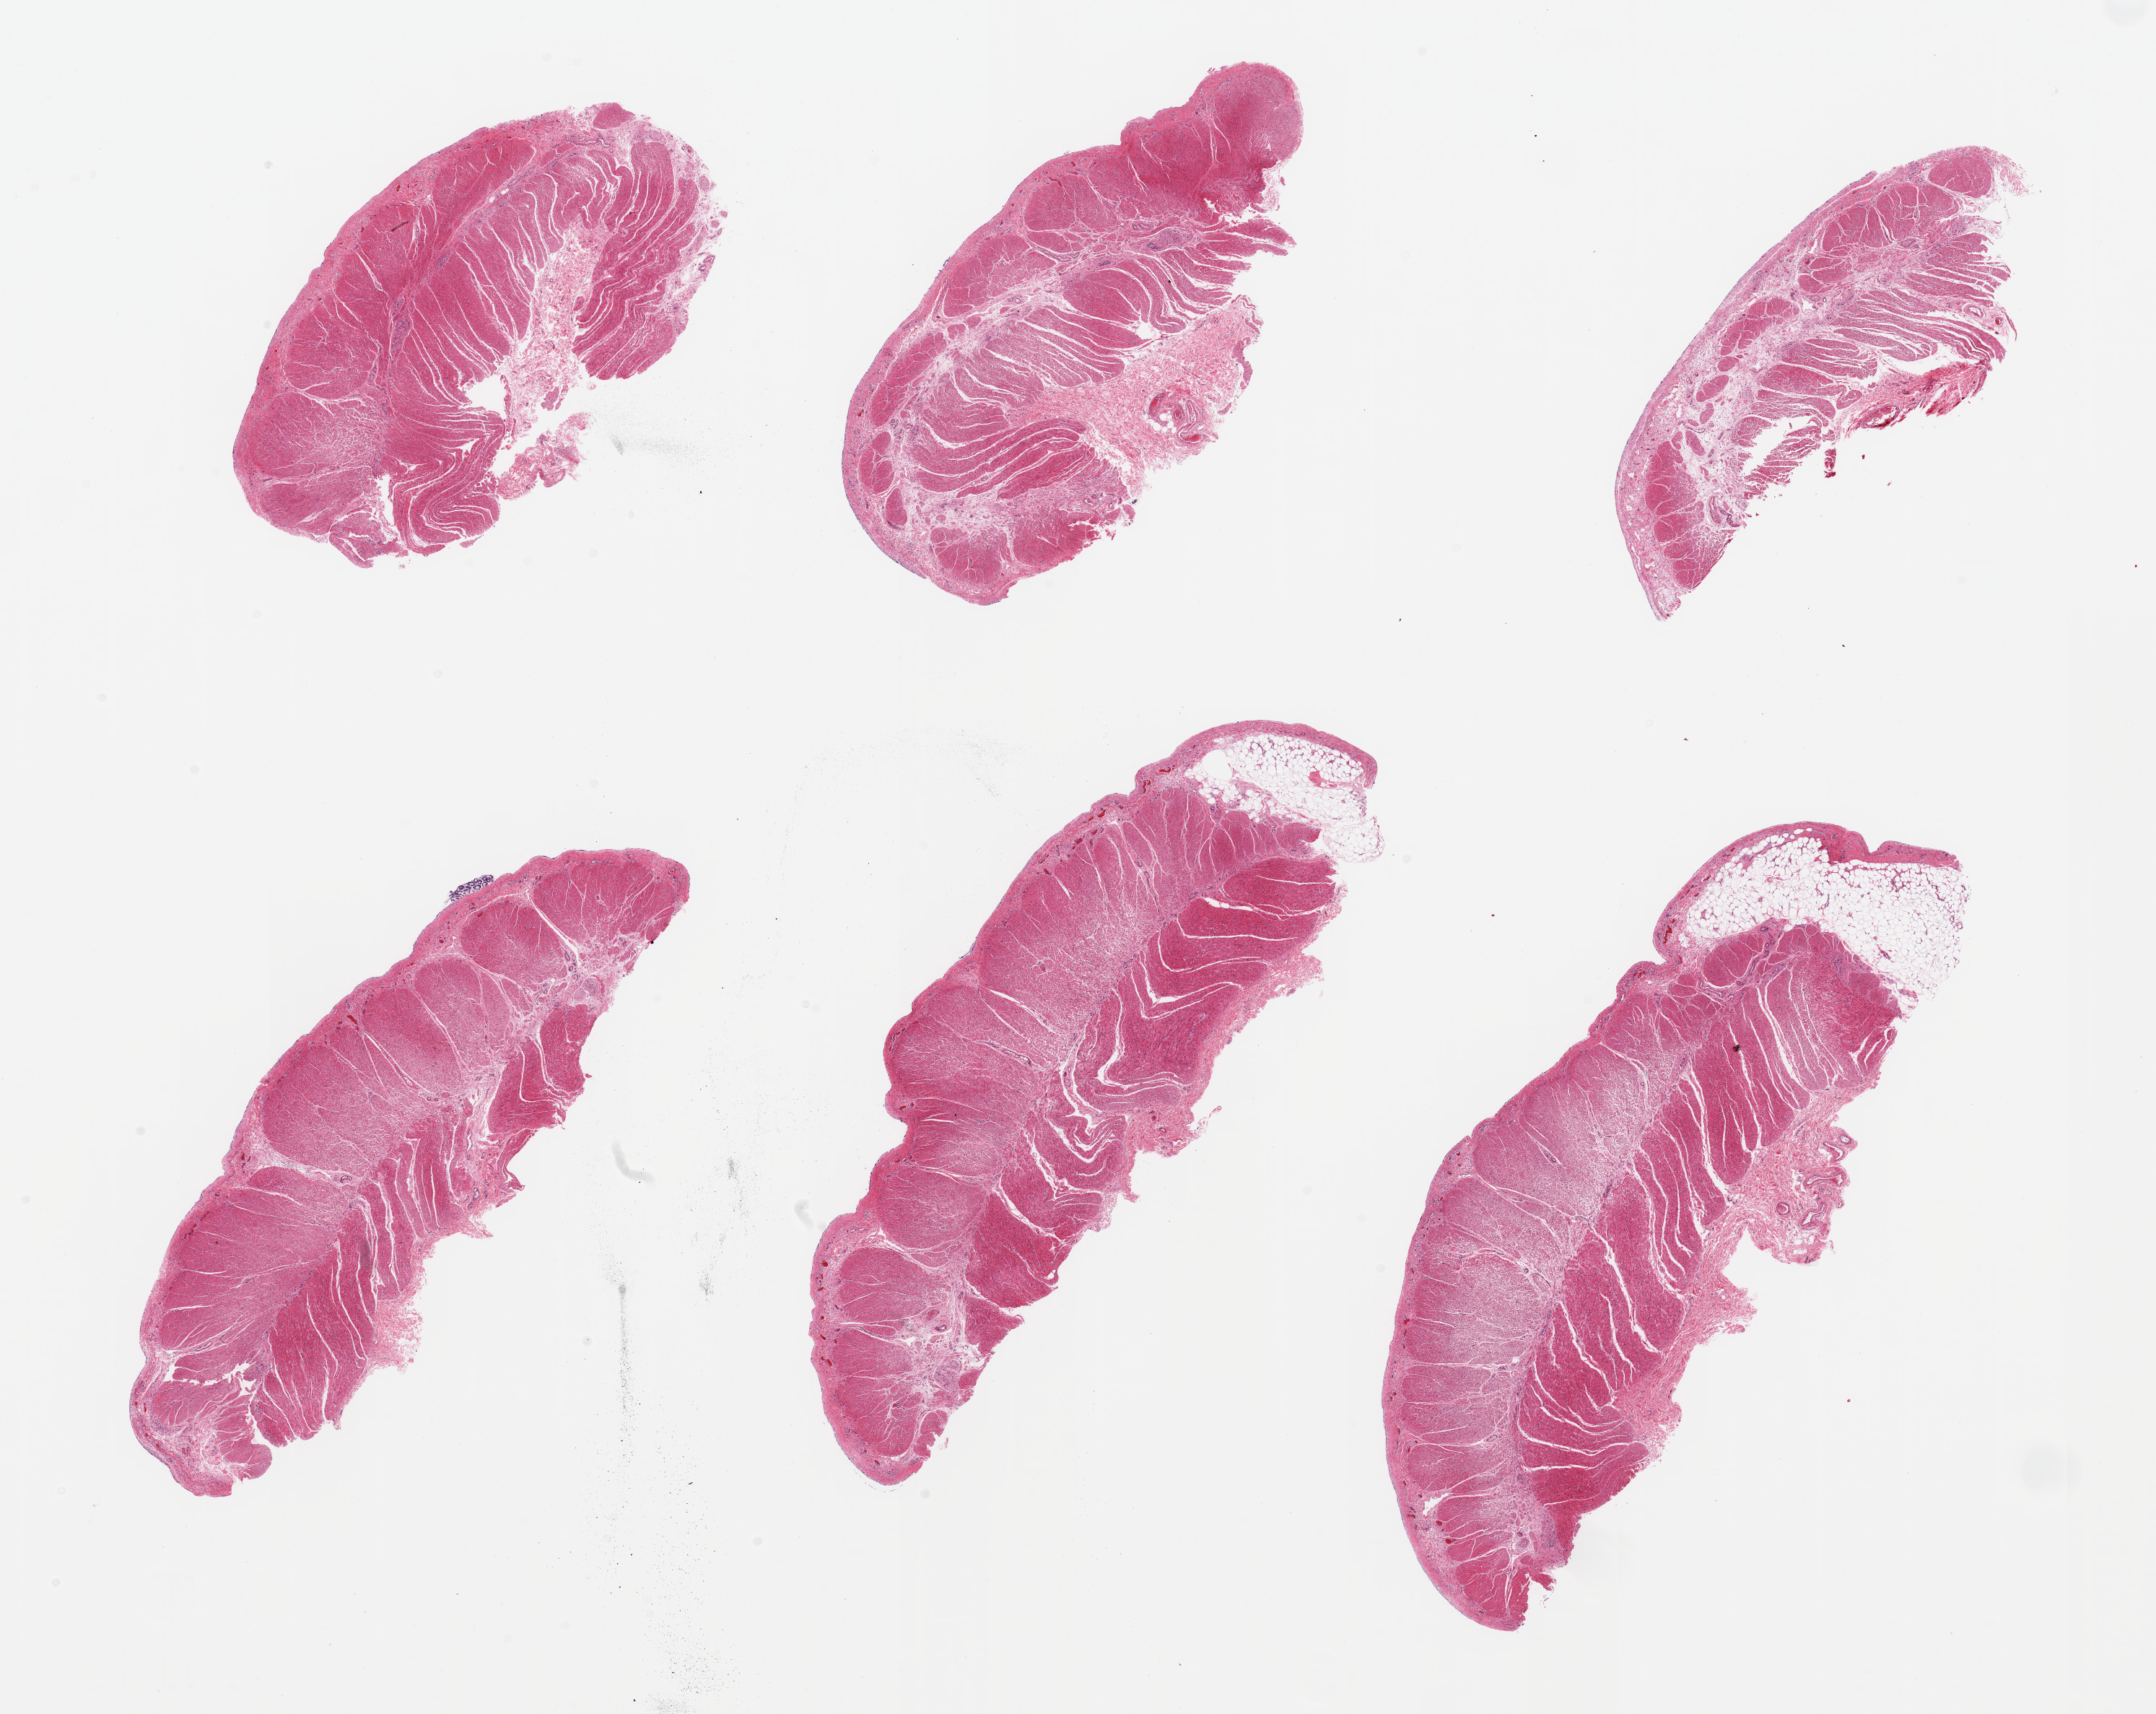
Whole-slide image, H&E stain — shown as a low-resolution overview of the whole scanned area (about 23.6 x 18.8 mm), PAXgene-fixed paraffin-embedded (PFPE) section, sampled site (target tissue): sigmoid colon, tissue donor sample.
- pathologist's review note for this sample: 6 pieces, confirmed target muscularis; nubbins of adherent fat up to ~1mm, prominent fibrosing mesothelial hyperplasia